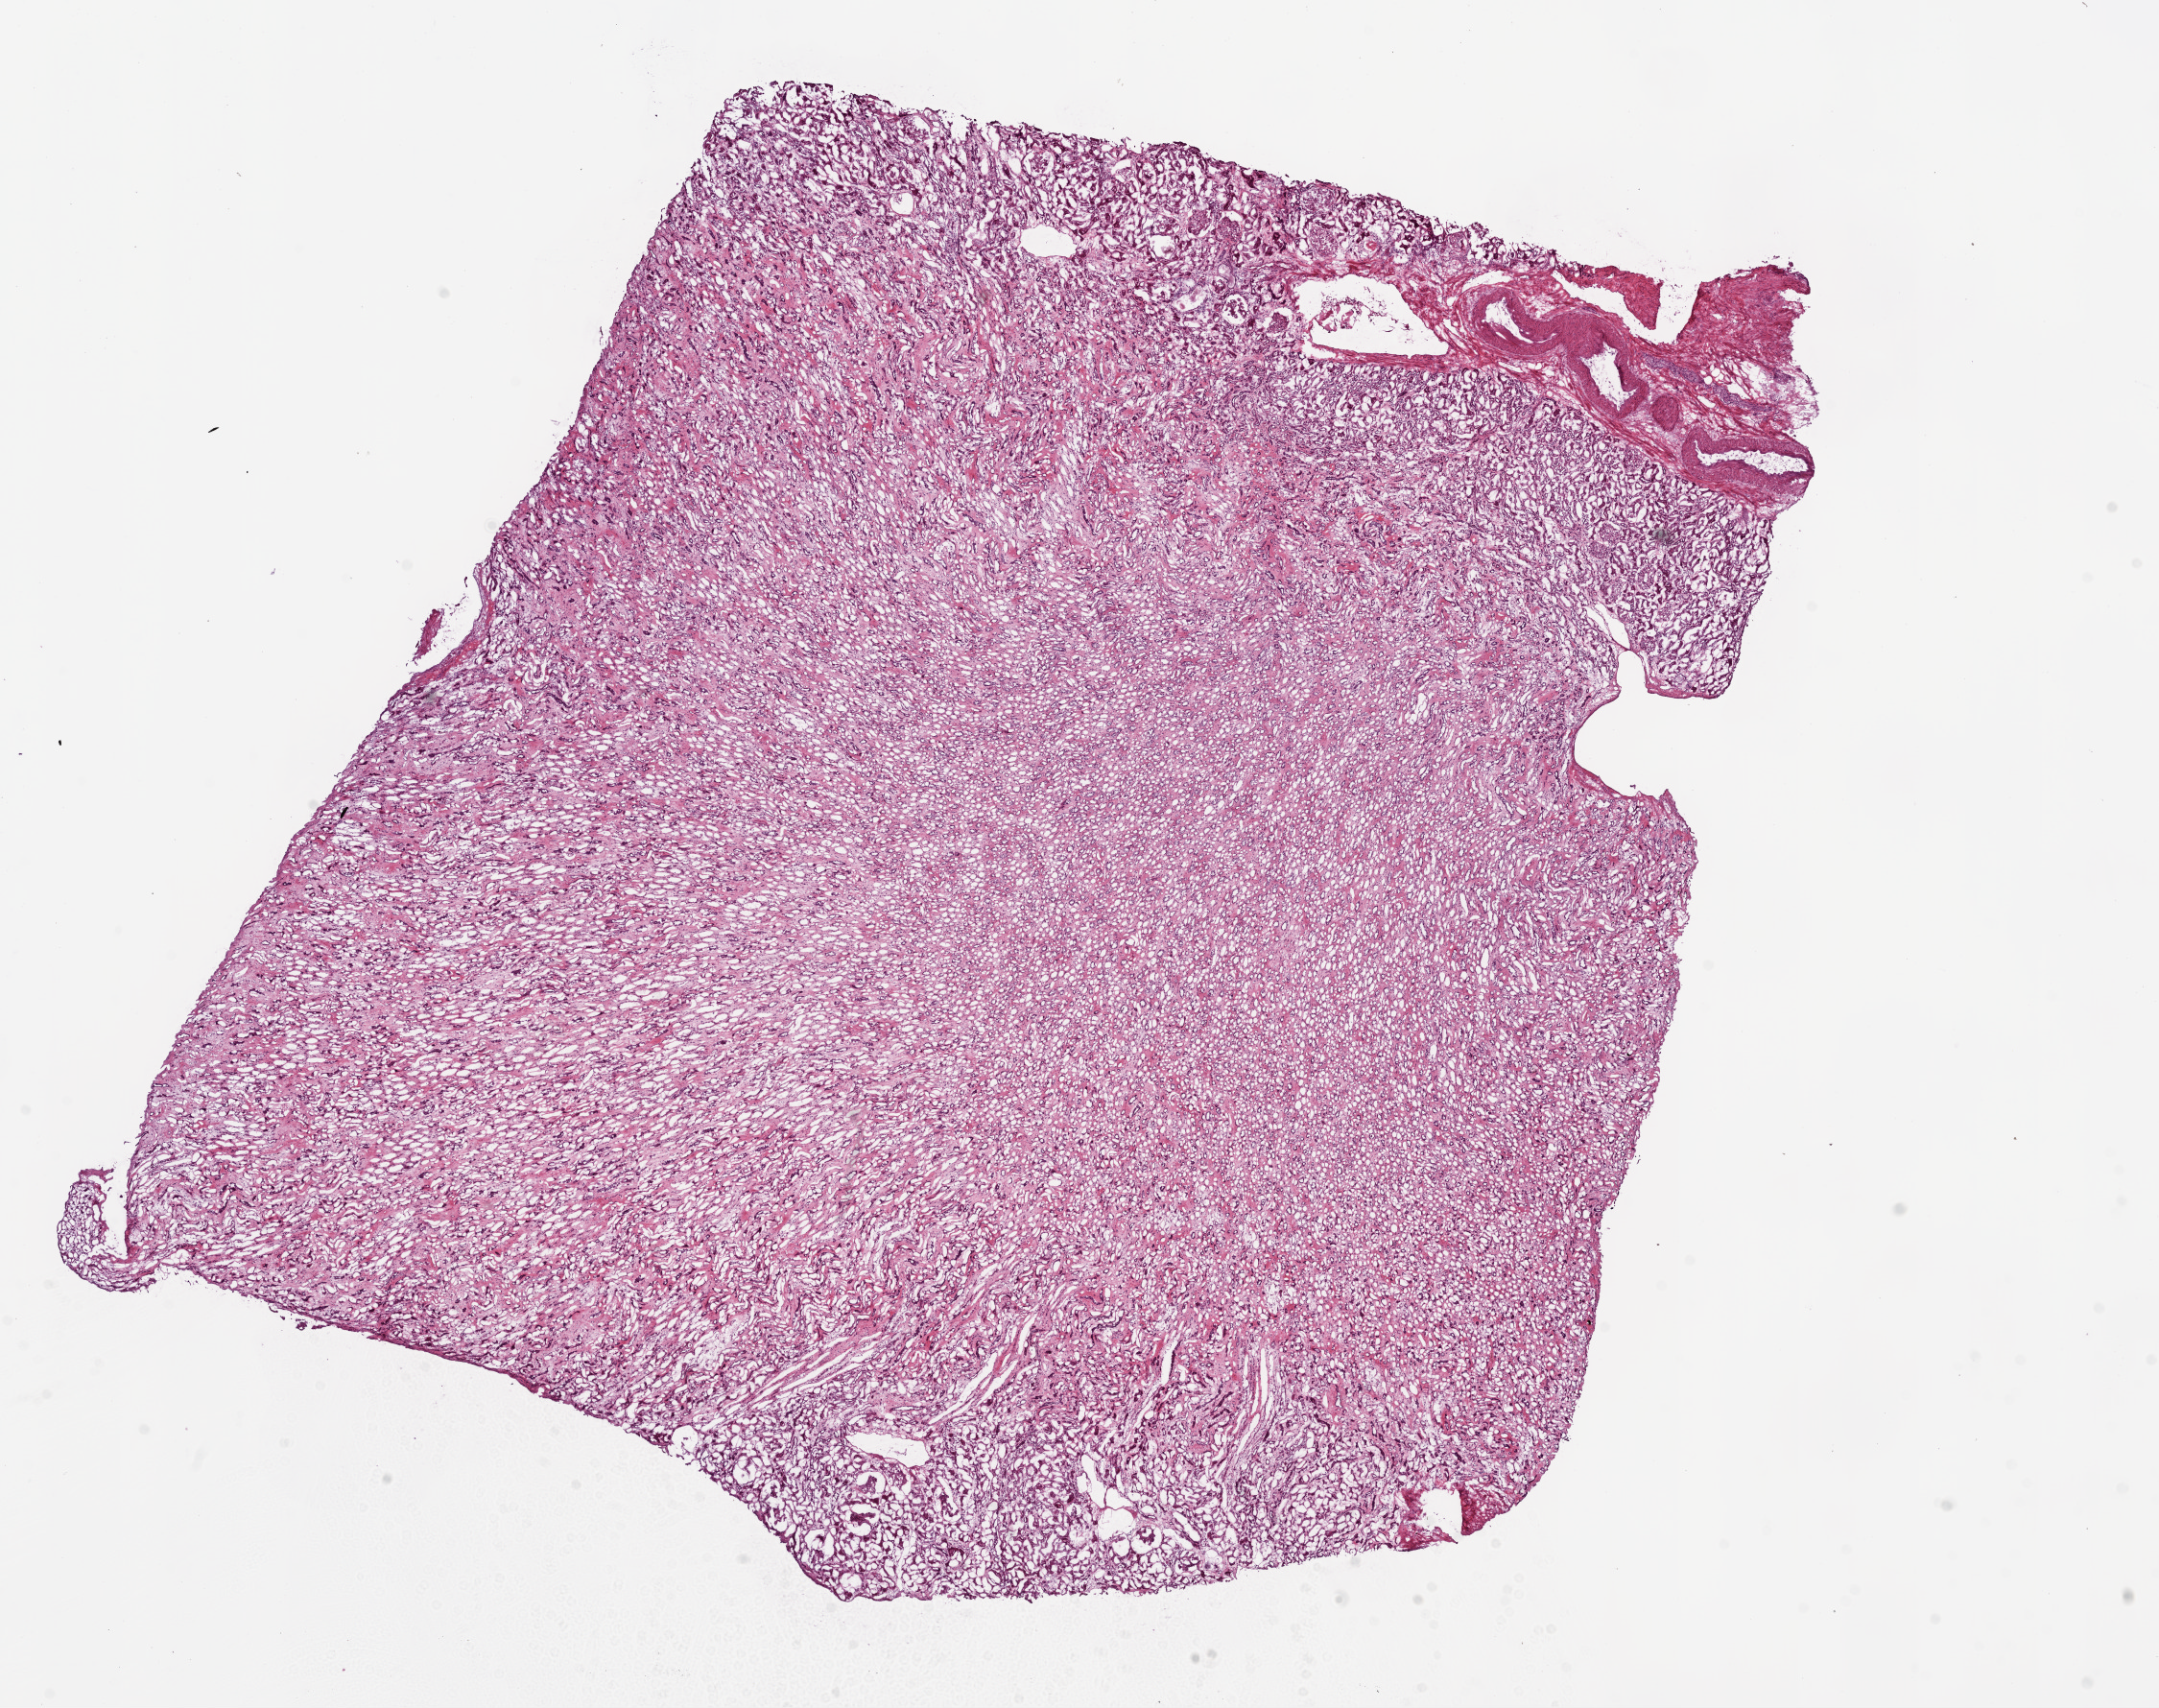
Whole-slide histology image, H&E, shown as a low-resolution overview of the whole scanned area (about 18.1 x 14.3 mm), frozen section from the bottom of the tissue portion, sample: solid tissue normal (non-tumour tissue), kidney. Male patient; age at initial diagnosis 82 years.
• this section: solid tissue normal sample (biorepository sample class)
• patient diagnosis: Clear cell adenocarcinoma, NOS